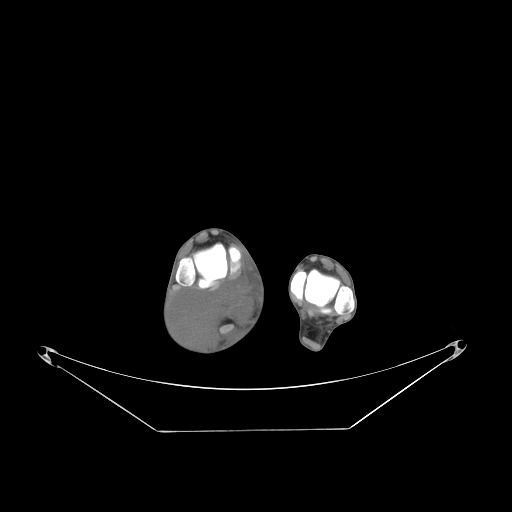
CT of an extremity soft-tissue mass (from a PET/CT study), one axial slice; slice 46 of 267 in the series (ordered by position); reconstruction kernel STANDARD; soft-tissue window (W 400 / L 40 HU); 3.75 mm slice thickness; 512 × 512 image matrix, field of view 500 × 500 mm. Male patient. From the clinical record (not read from this slice): histological type: liposarcoma - round cell; grade: high; site of the primary tumour: right calf.
Annotated regions visible in this slice (expert contour drawn on MRI and transferred to this co-registered scan by the dataset authors):
- gross tumour volume (mass): bounding box [x1, y1, x2, y2] px = [171, 278, 257, 350]